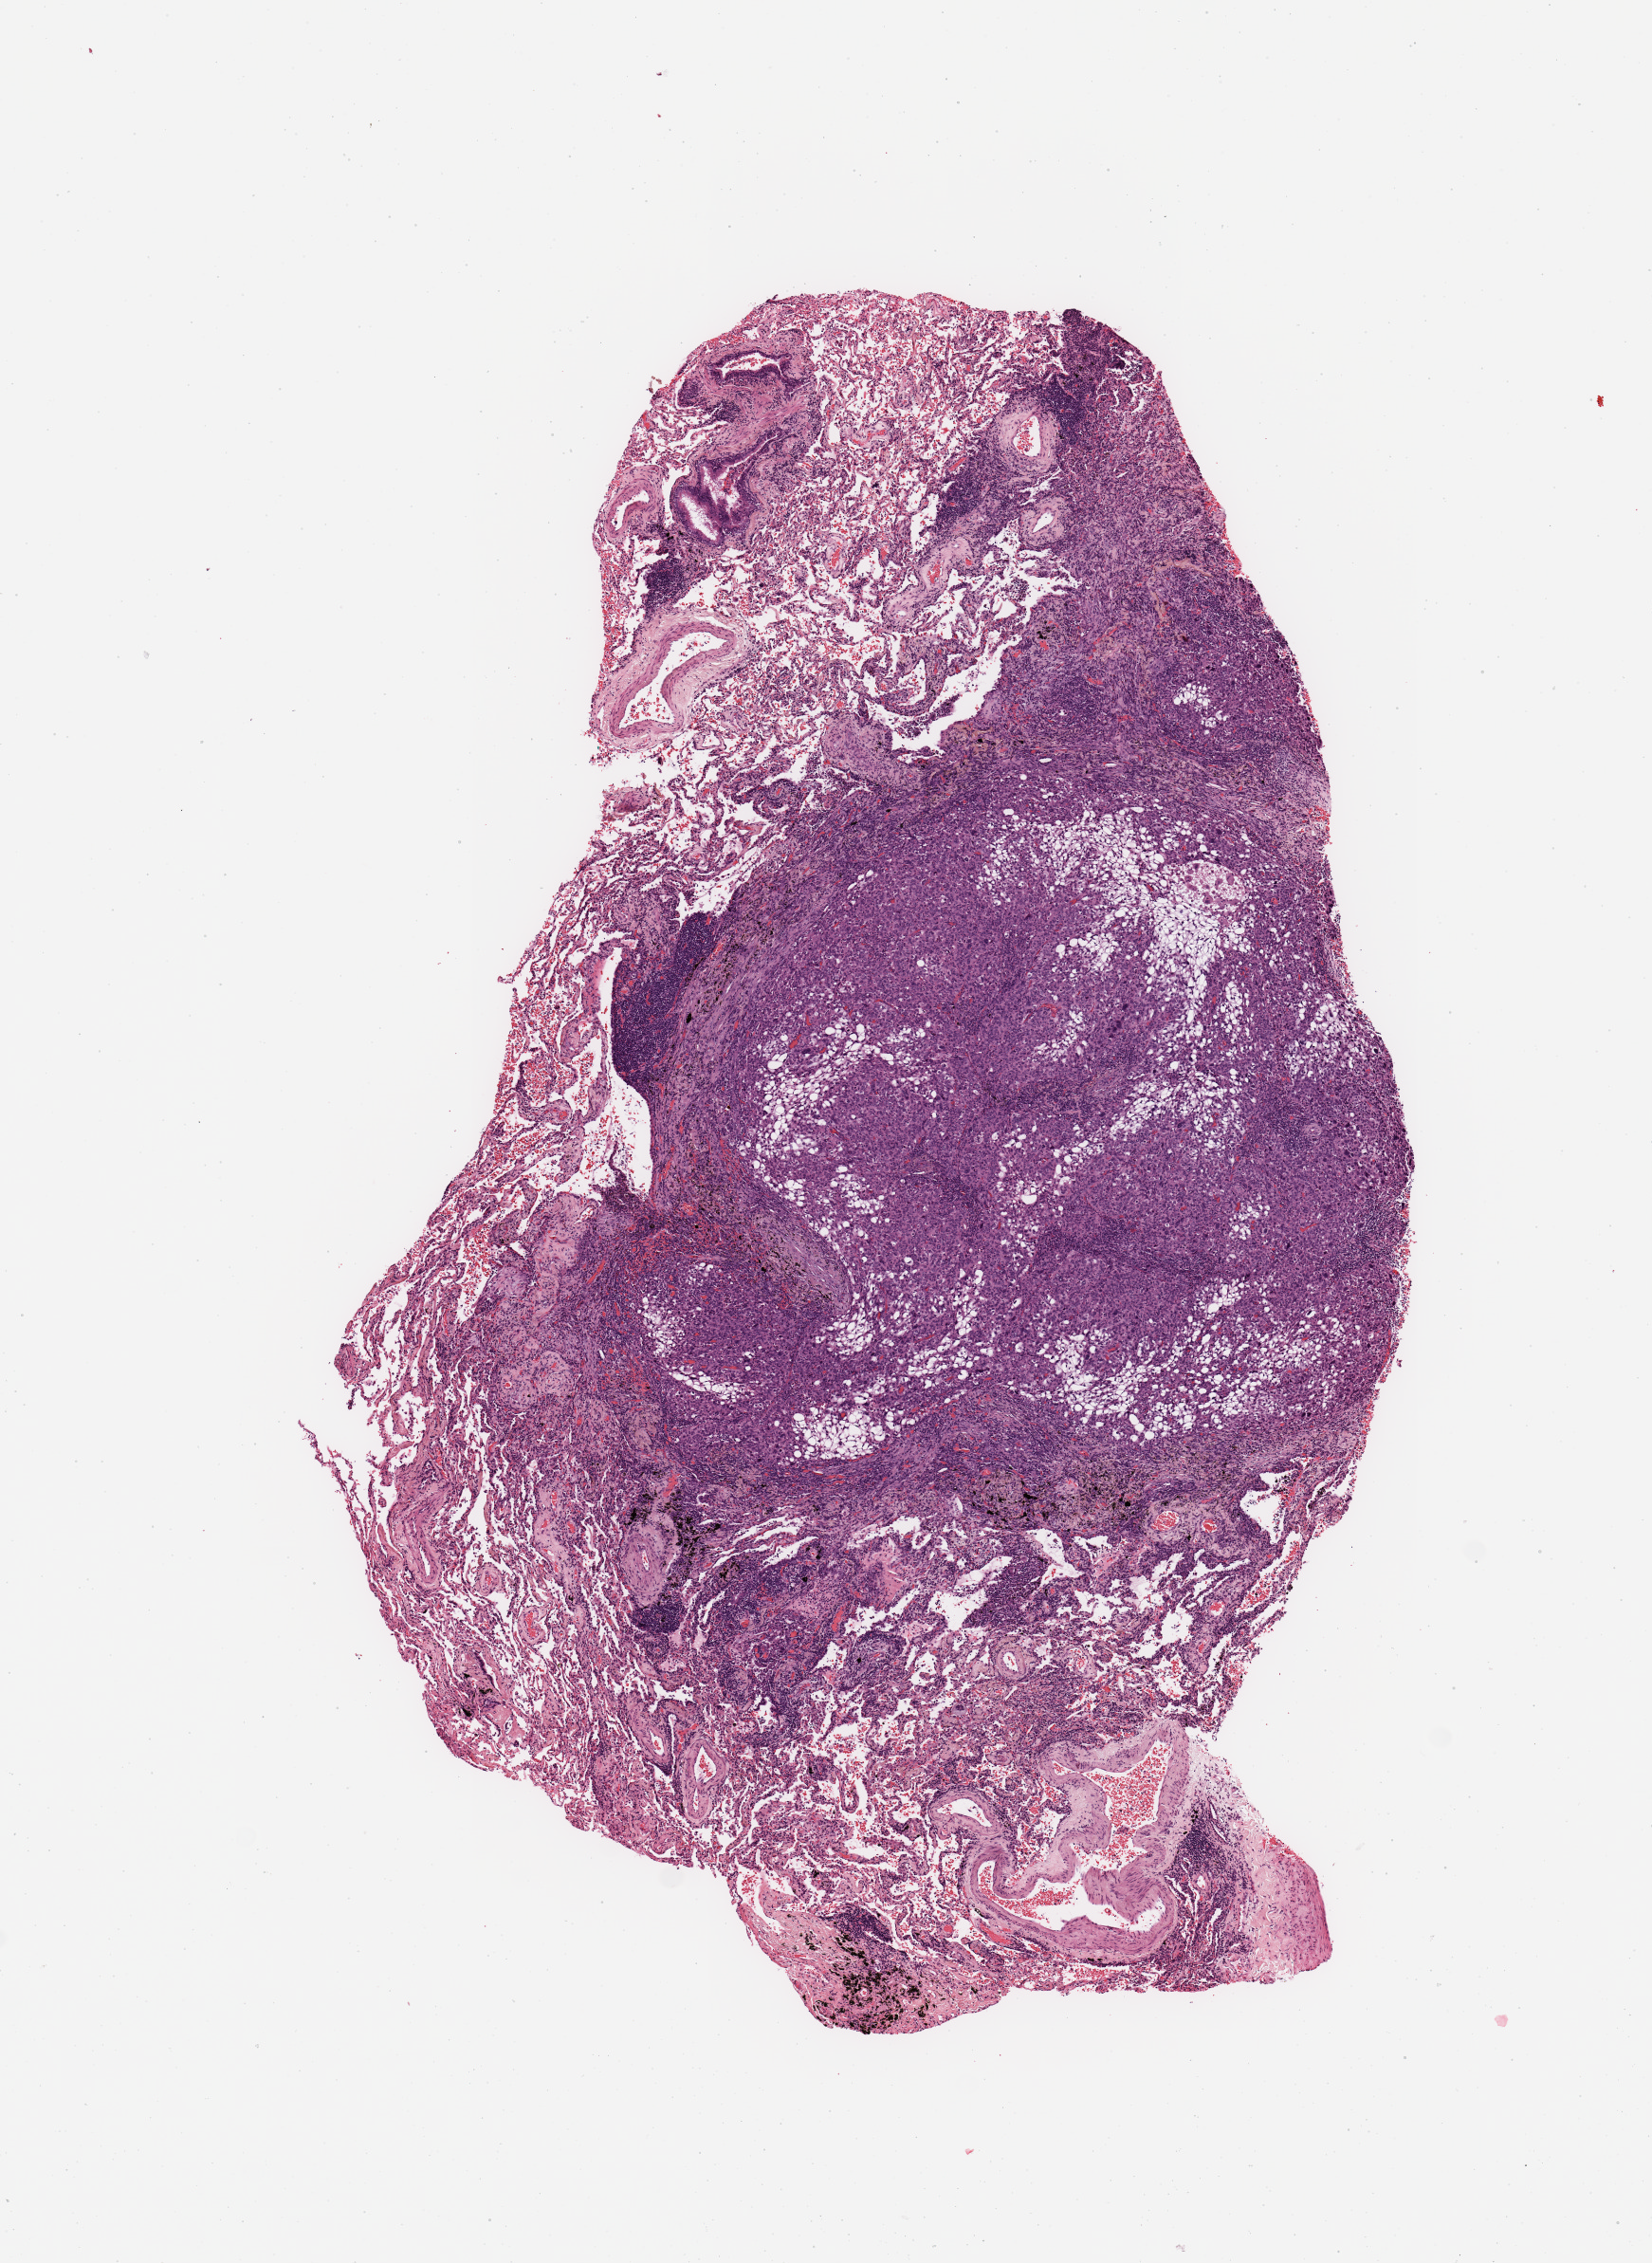
H&E whole-slide image, a low-resolution overview of the entire scanned area, about 6.9 x 9.4 mm. Tumour tissue sample, sampled site: lung. 76-year-old male patient. Histologic grade: G2 (moderately differentiated). Pathologist review of this section (percent, as recorded): tumour nuclei 65%, necrosis 5%.
Diagnosis: Squamous cell carcinoma, NOS. AJCC pathologic stage: IA3. Primary tumour site (as recorded): left upper lobe.